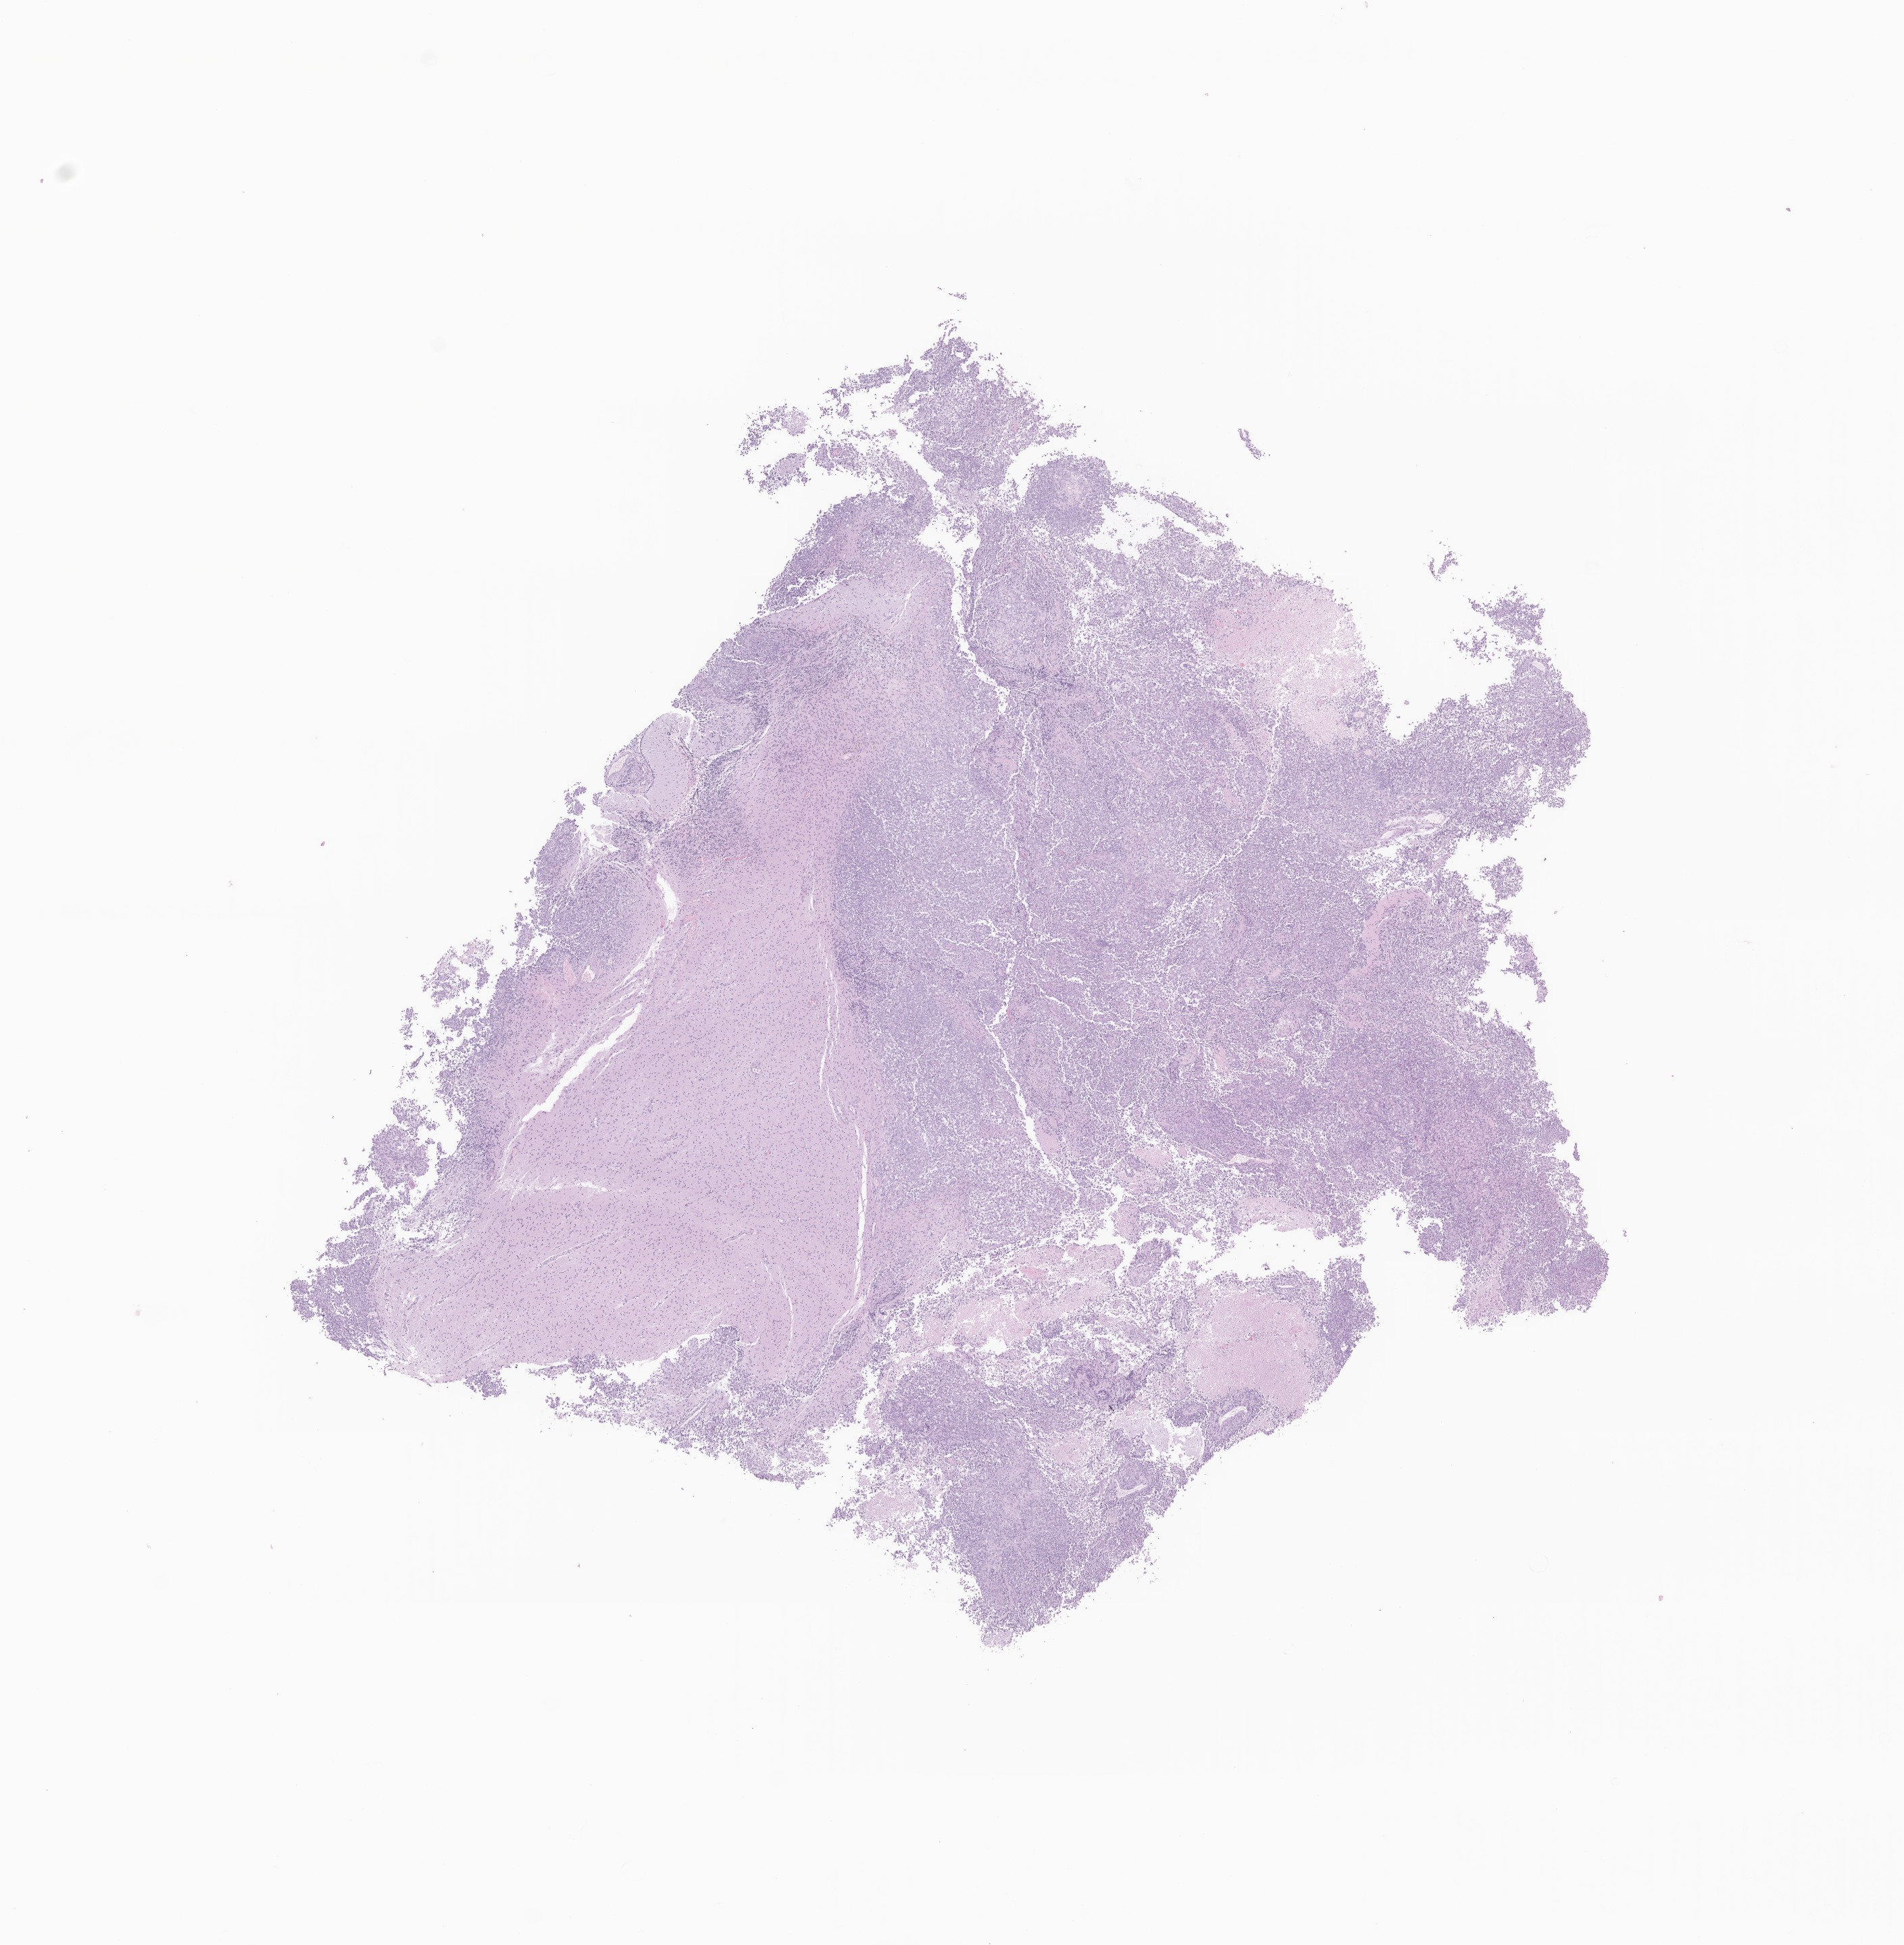
Digitized haematoxylin and eosin-stained section of tumor tissue from the brain, low-resolution overview of the scanned area, about 11.9 x 12.1 mm, formalin-fixed paraffin-embedded section. Patient: female, age 217 days.
- diagnosis (ICD-O-3 morphology term): Atypical teratoid/rhabdoid tumor